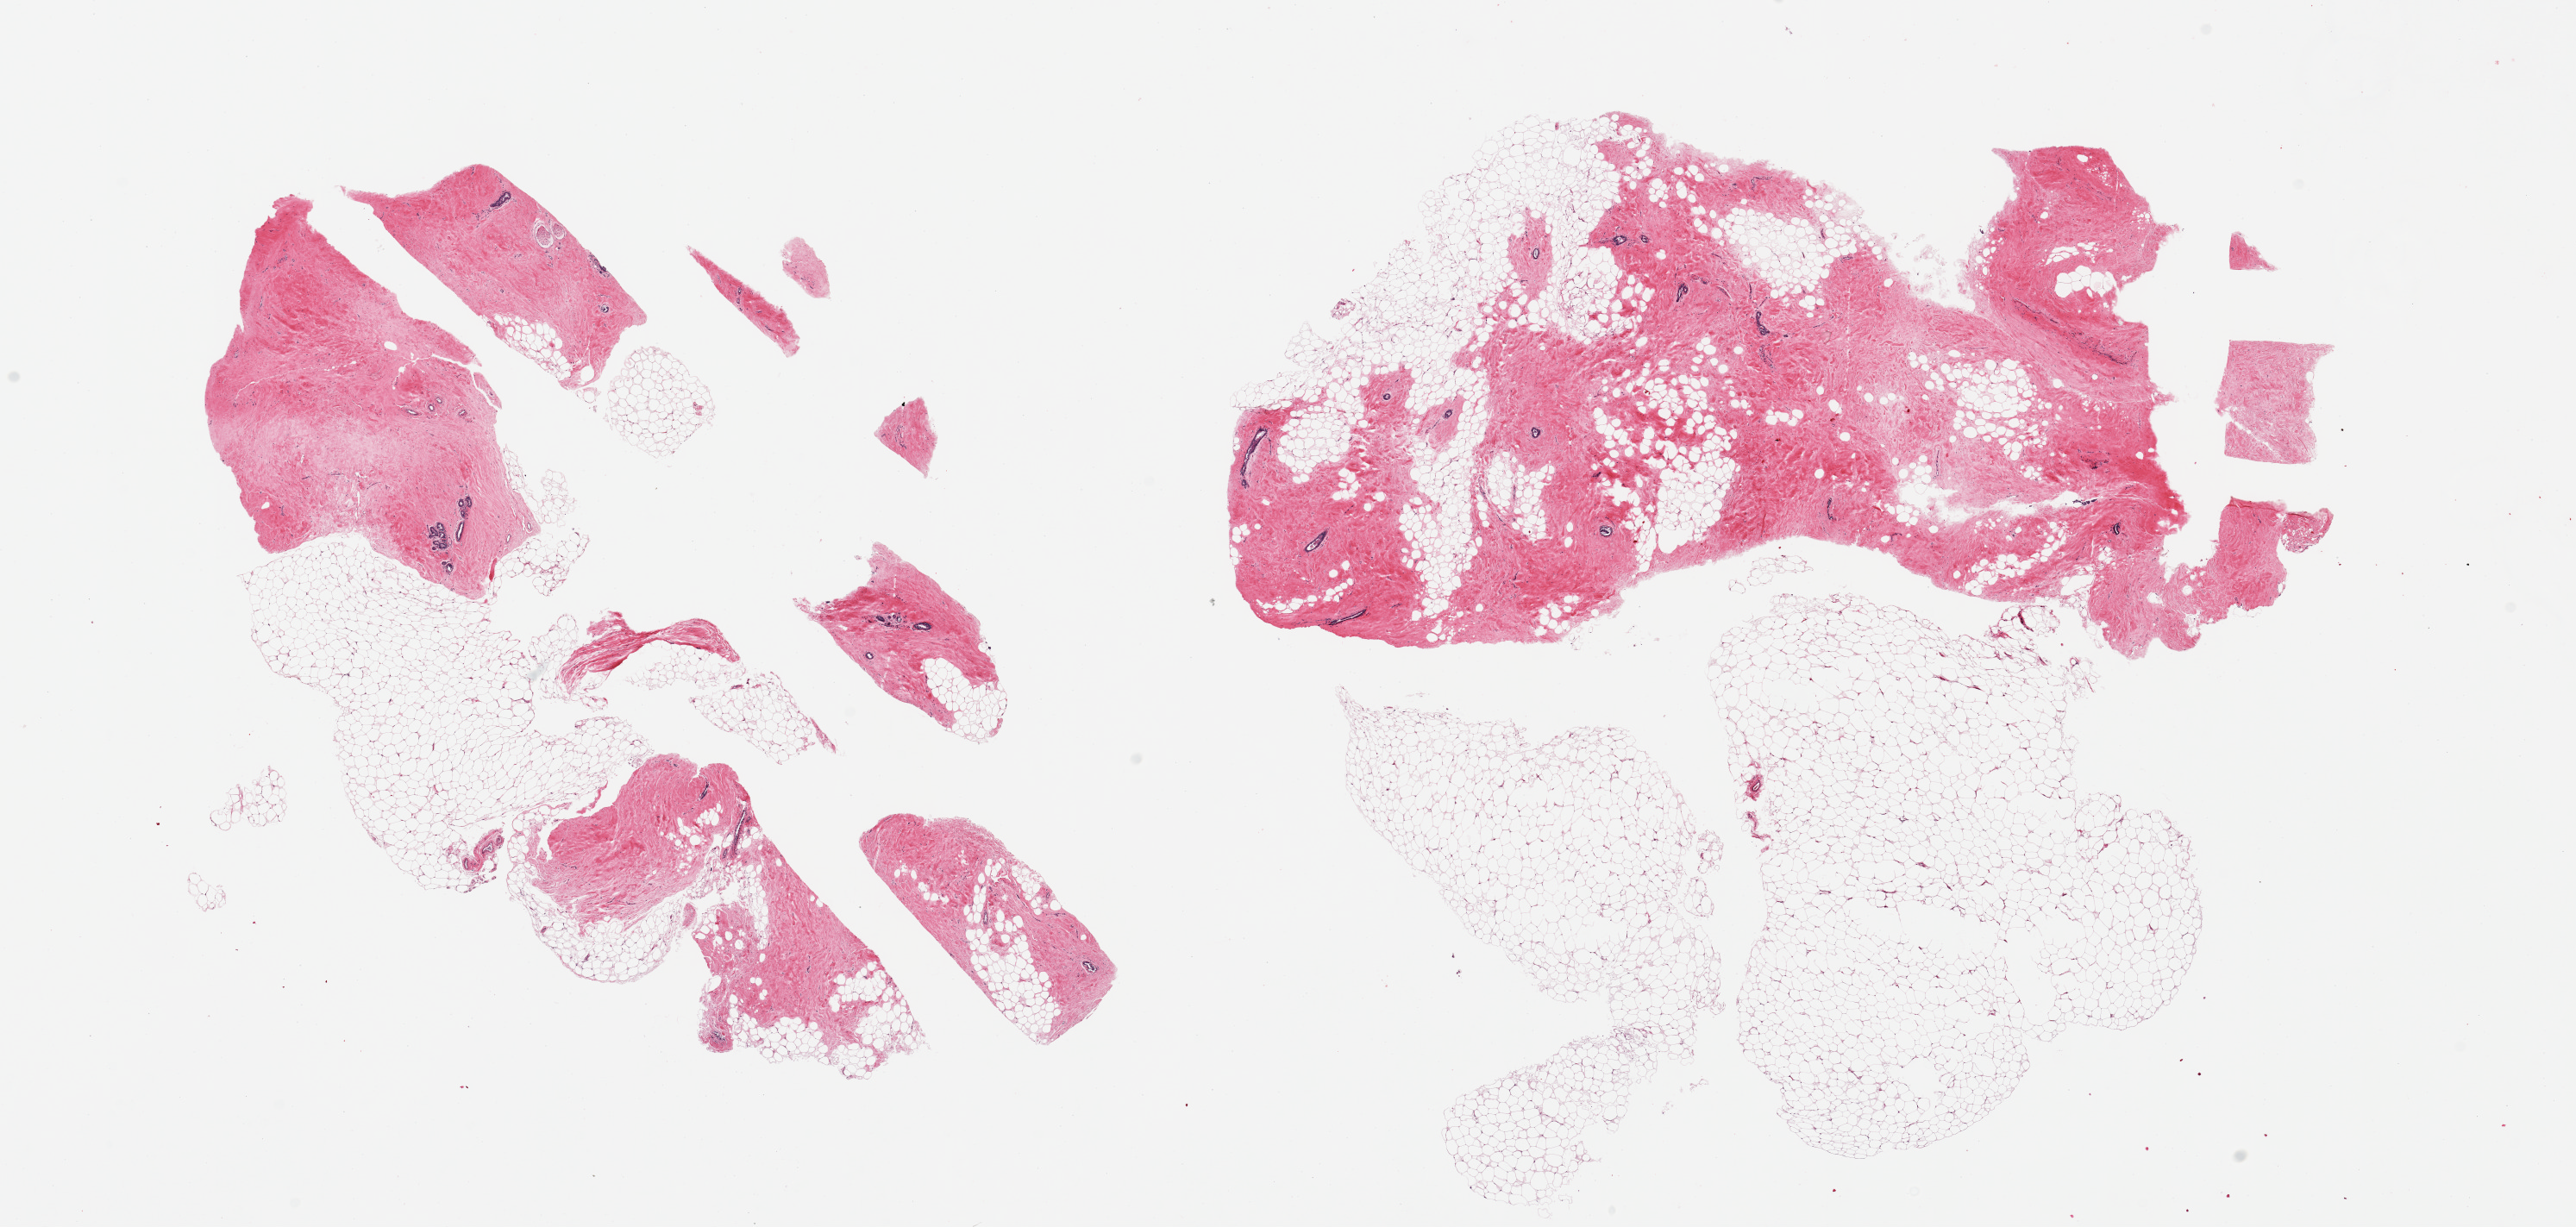
Digitized haematoxylin and eosin-stained section, shown as a low-resolution overview of the whole scanned area (about 23.6 x 11.3 mm), PAXgene-fixed, paraffin-embedded tissue, target tissue: breast, donor tissue sample.
- pathologist's review note for this sample: 2 pieces (fragmented); 30 and 60% adipose tissue with dense fibrous stroma with scattered ductal structures